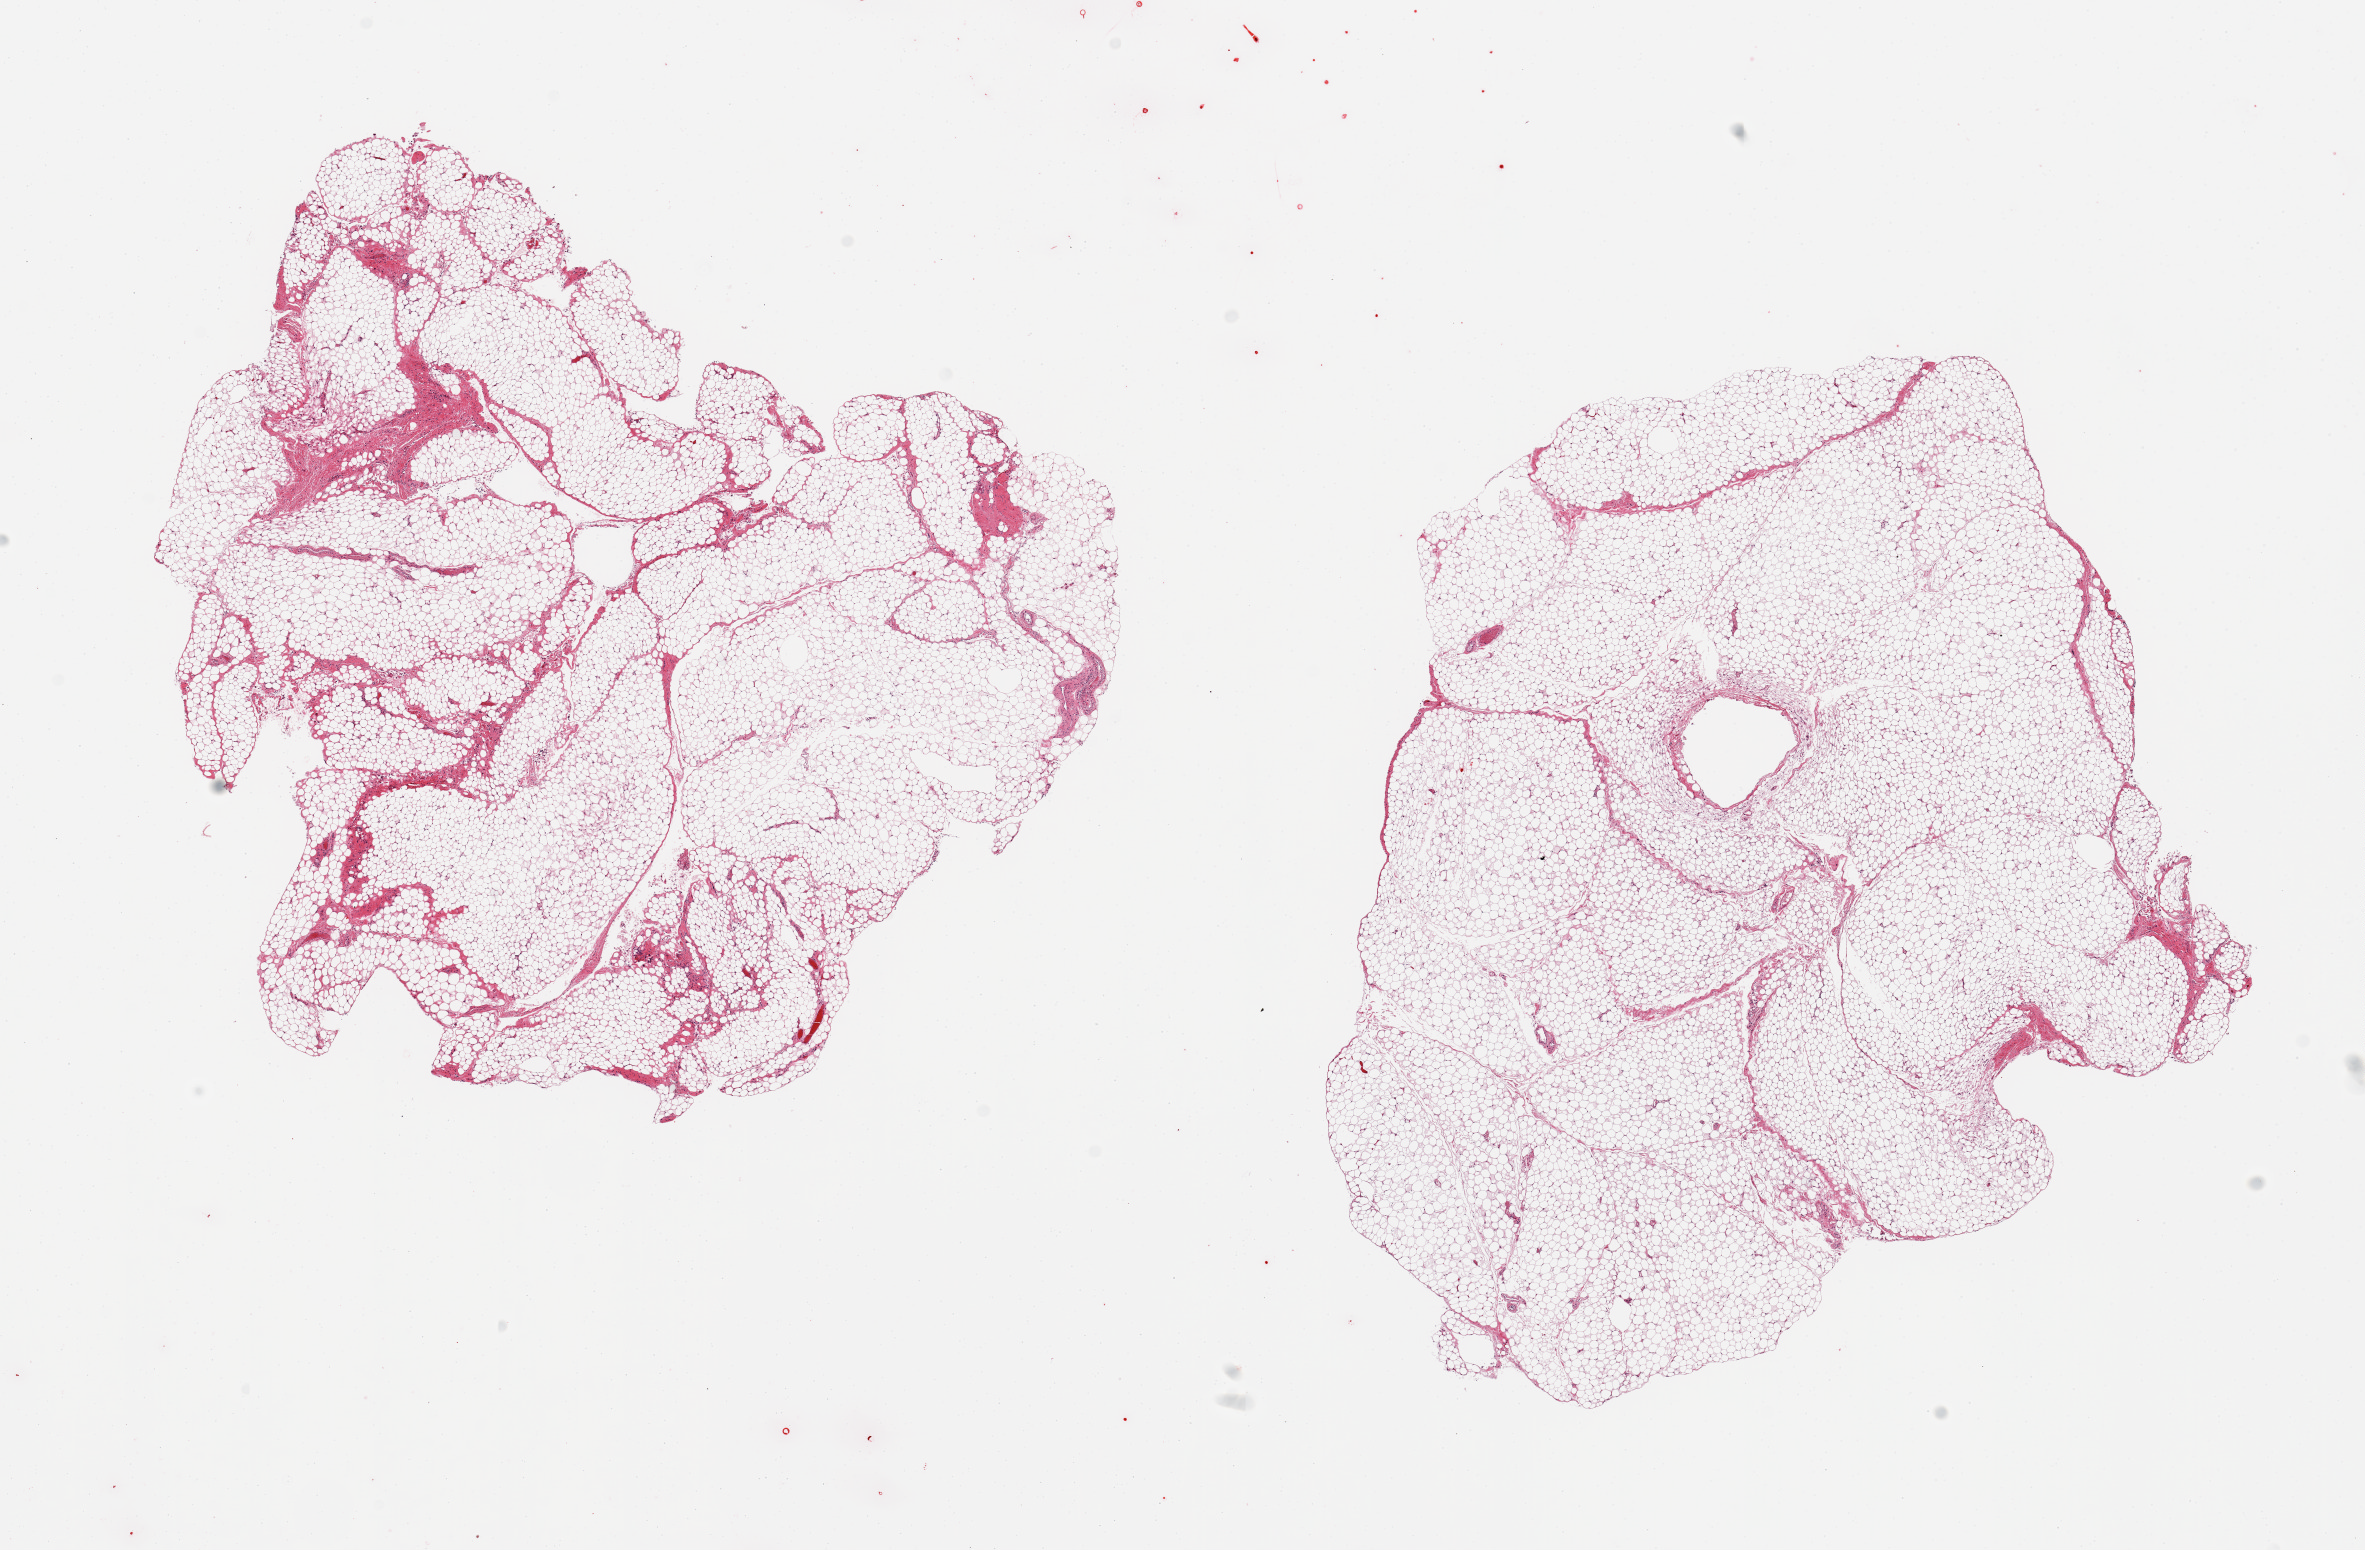
Hematoxylin and eosin (H&E) whole-slide image, brightfield, shown as a low-resolution overview of the whole scanned area (about 18.7 x 12.3 mm, acquisition: 20x scan), PAXgene-fixed, paraffin-embedded tissue, sampled site (target tissue): omentum, donor tissue sample.
Reviewer comment on this tissue sample: 2 pieces, patchy fascia/vascular elements, ~10-15%.